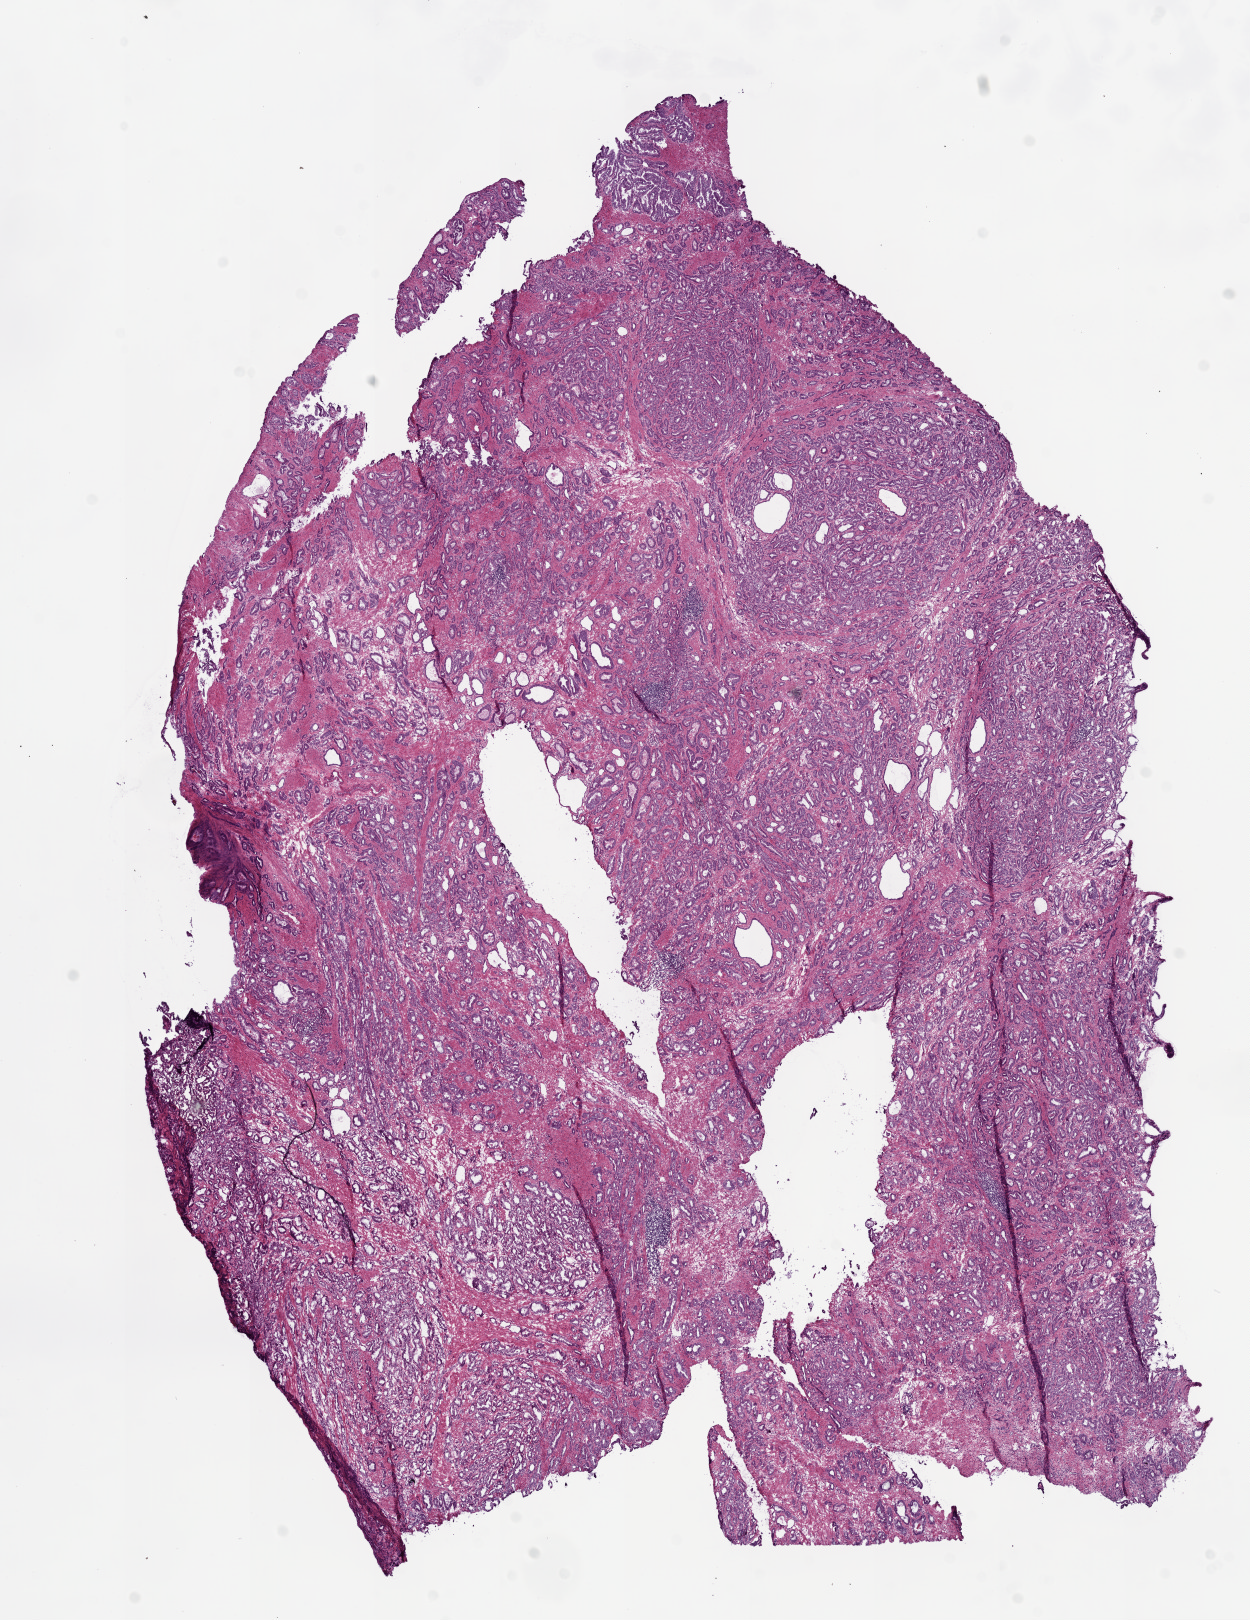
Whole-slide histology image, H&E, a low-resolution overview of the entire scanned area, about 10.0 x 13.0 mm, frozen section, primary tumour sample from the prostate. Male, age 55 years at initial diagnosis. Gleason score: 6 (3+3). Slide review estimates, as recorded: tumour cells 75%, tumour nuclei 75%, normal cells 5%, stromal cells 20%, necrosis 0%. Infiltration values recorded for this section: lymphocyte infiltration 5%, monocyte infiltration 0%, neutrophil infiltration 0%.
Diagnosis: Acinar cell carcinoma (prostate gland).